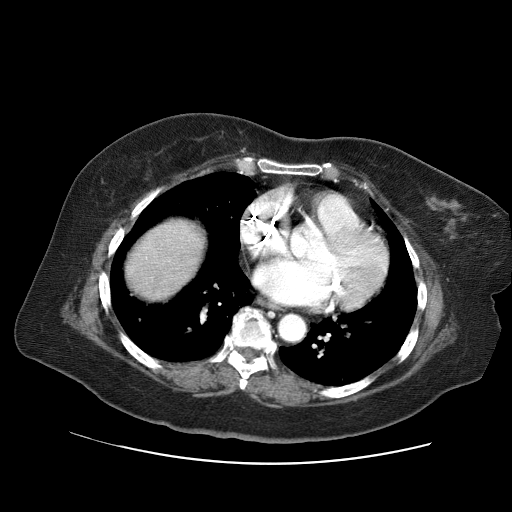
Contrast-enhanced abdominal CT (liver protocol), one axial slice; position 65 of 71 along the scan axis; reconstruction kernel STANDARD; 120 kVp; soft-tissue window (W 400 / L 40 HU); 2.5 mm slice thickness; 512 × 512 image matrix, field of view 400 × 400 mm. From the clinical record (not read from this slice): diagnosis: hepatocellular carcinoma (patient treated with transarterial chemoembolisation; whether this scan precedes or follows treatment is not stated here); TNM stage (as recorded): Stage-II; Child-Pugh class: A; tumour differentiation: poorly differentiated; tumour nodularity: multinodular.
Structures marked on this image (semi-automatic segmentation, software-assisted and operator-edited):
- abdominal aorta: bounding box <278,315,303,338> (left, top, right, bottom; pixels)
- liver parenchyma outside the tumour (the mass and vessels are separate outlines, so this box may not span the whole liver): <126,218,204,298>